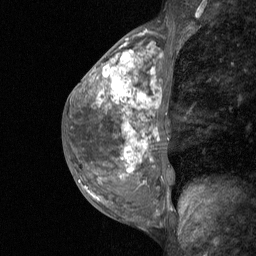
Breast MRI (dynamic contrast-enhanced), one sagittal slice. Position 27 of 64 along the scan axis. Dynamic contrast-enhanced study with each time point stored as its own series, time point 2 of 3 at this slice position (early post-contrast, ordered by acquisition time). 1.5 T. TE 4.8 ms, TR 27 ms. 2 mm slice thickness. 256 × 256 image matrix. Female patient, age 36 years. Case-level facts recorded for this patient, not image findings: setting: breast cancer imaged before/during neoadjuvant chemotherapy; receptor status: HR-positive, HER2-negative.
Outlined on this slice (semi-automatic segmentation, software-assisted and operator-edited):
- analysis volume of interest (the breast-tissue region the enhancement analysis was run in; not a lesion): box from (x=73, y=54) to (x=173, y=210) px
- tumour enhancement mask (voxels above the 90 % enhancement threshold inside the analysis volume of interest): (x=104, y=60)–(x=131, y=82)